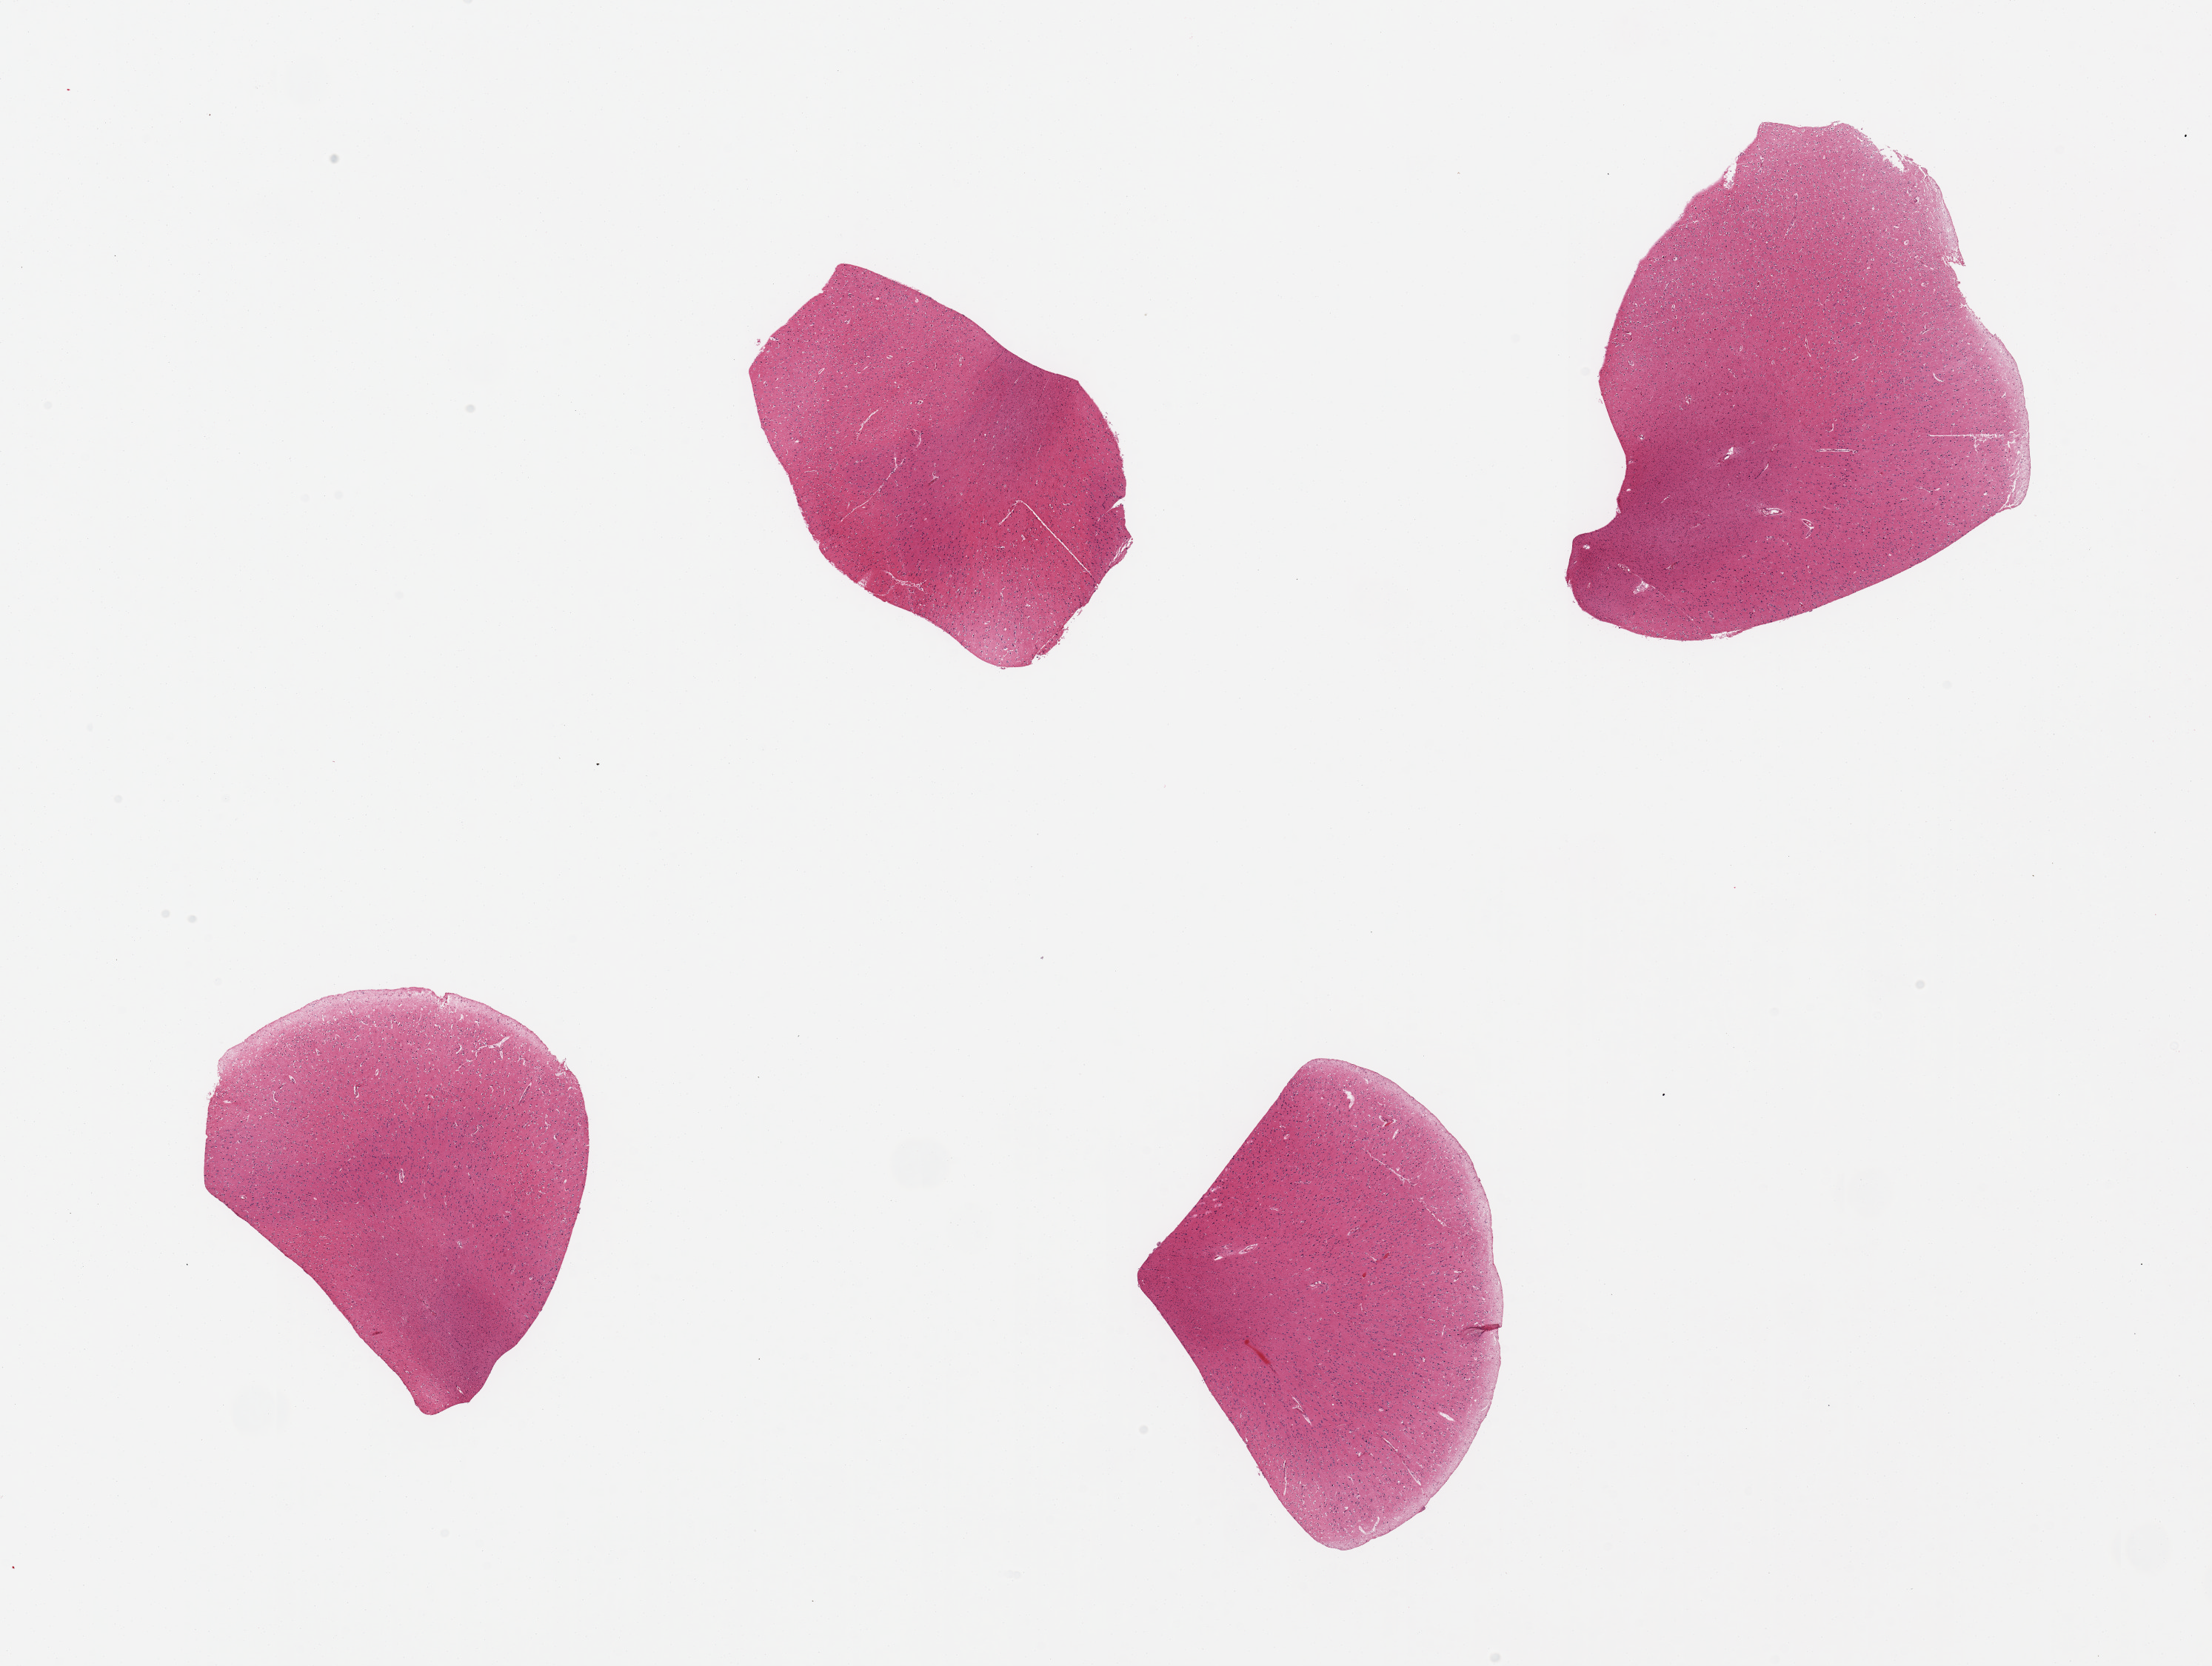
Digitized hematoxylin and eosin (H&E)-stained section — low-resolution overview of the scanned area, about 23.6 x 17.8 mm. PAXgene-fixed, paraffin-embedded tissue. Section of cerebral cortex (target tissue). Tissue donor sample.
Reviewer comment on this tissue sample: 4 pieces.